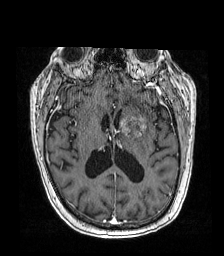
Brain MRI from a brain-tumour surgery series, one axial slice. Position 81 of 192 along the scan axis. T1-weighted post-contrast. 1 mm slice thickness. 224 × 256 image matrix, field of view 219 × 250 mm. From the clinical record (not read from this slice): histopathology: Metastatic carcinoma from lung primary; tumour location: Left Frontal Caudate.
Outlined on this slice (expert manual segmentation):
- tumour: bounding box <117,114,148,137> (left, top, right, bottom; pixels)